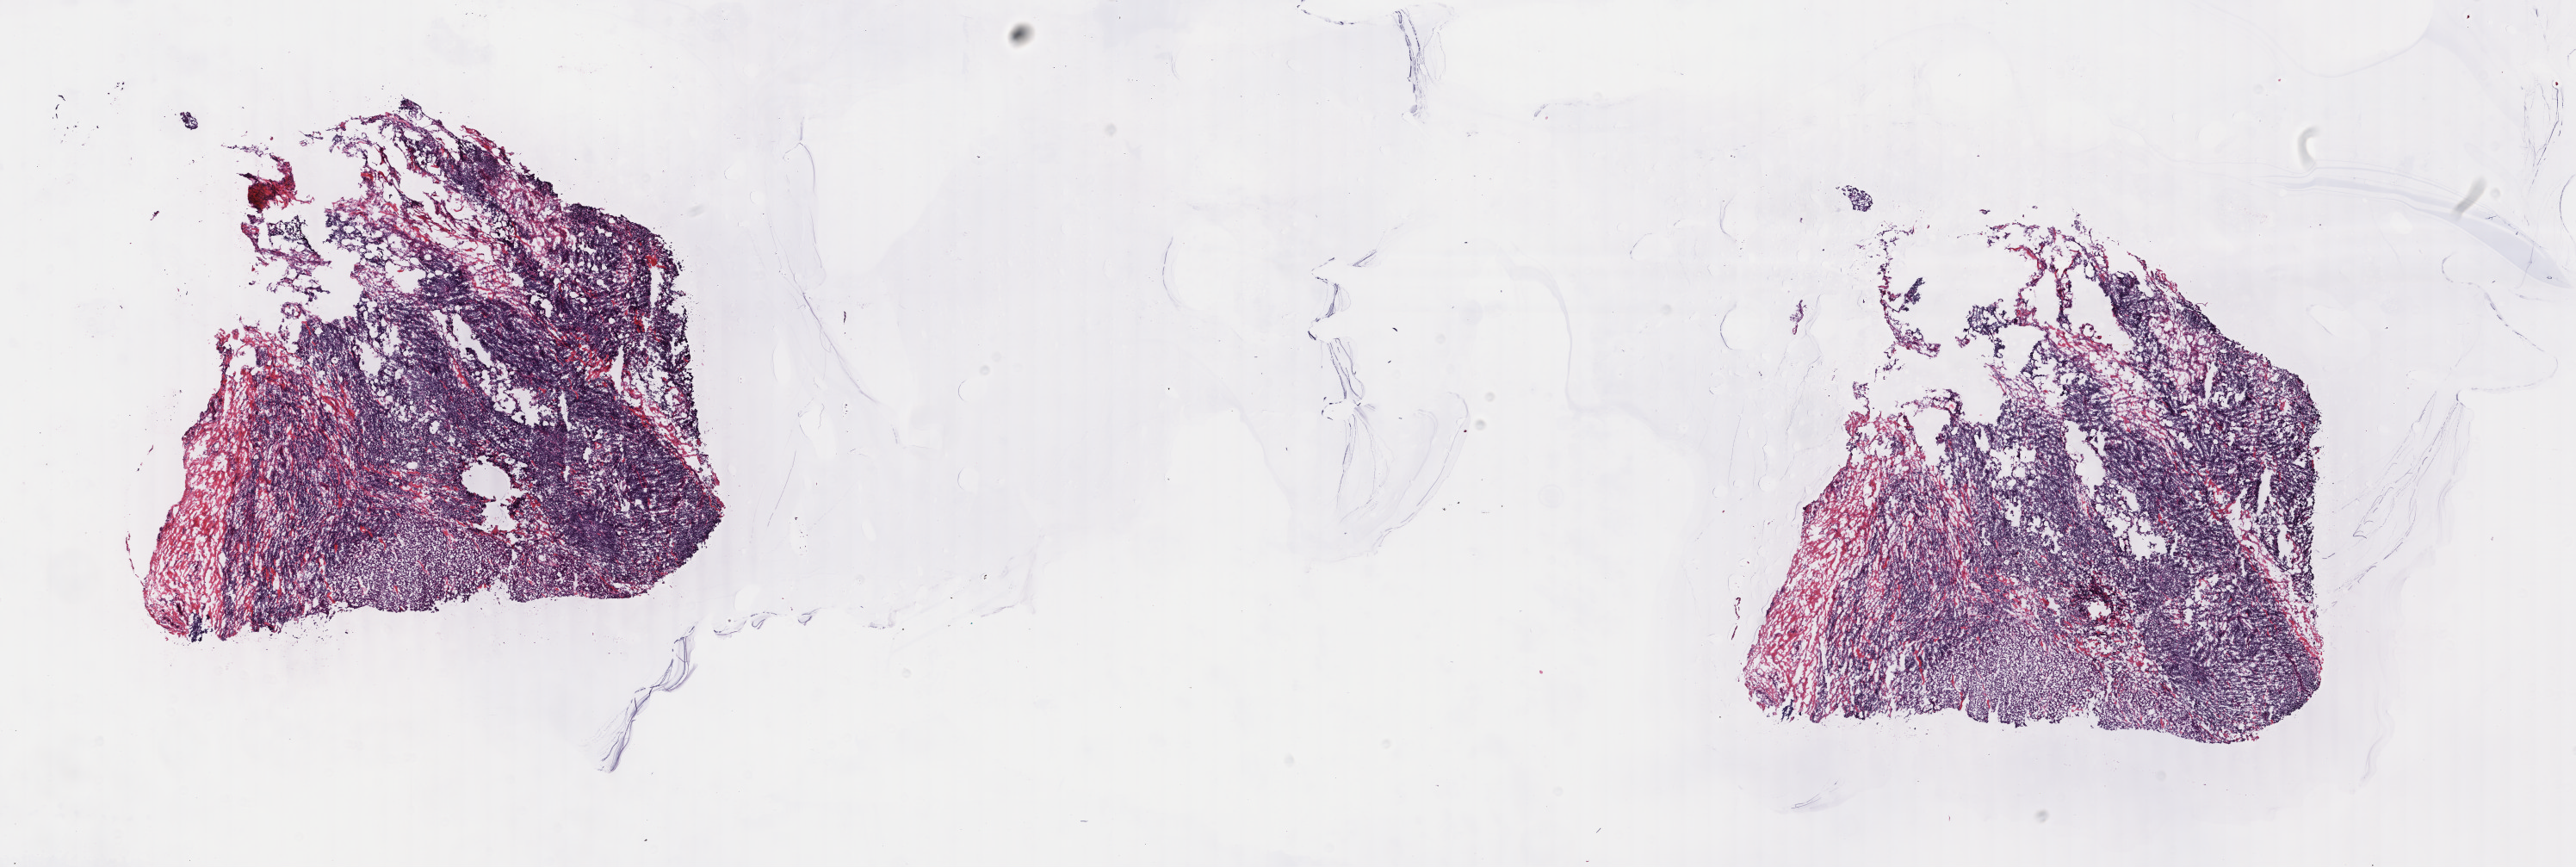
Whole-slide histology image, H&E — a low-resolution overview of the entire scanned area, about 23.8 x 8.0 mm (slide scanned at 40x). Frozen section from the bottom of the tissue portion. Sample: primary tumour, breast. Female, age 64 years at initial diagnosis. Pathologist review of this section (percent, as recorded): tumour cells 90%, tumour nuclei 90%, normal cells 0%, stromal cells 10%, necrosis 0%. Inflammatory infiltration, as recorded: lymphocyte infiltration 1%, monocyte infiltration 0%, neutrophil infiltration 0%.
Lymph nodes positive (case pathology): 0 of 12 examined. AJCC pathologic stage: IIA. Histologic diagnosis: Infiltrating duct carcinoma, NOS. Laterality: right.